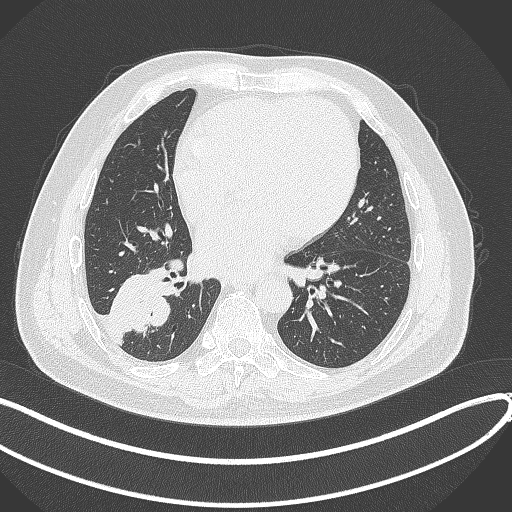
Chest CT, one axial slice; position 150 of 360 along the scan axis; reconstruction kernel B70f; 120 kVp; lung window (W 1500 / L -600 HU); 1 mm slice thickness; 512 × 512 image matrix, field of view 400 × 400 mm. Male patient, age 59 years.
Annotated regions visible in this slice (rectangle marked by the reading radiologist):
- lung tumour (recorded histology: adenocarcinoma): bounding box (x1, y1, x2, y2) in pixels: (109, 258, 173, 336)